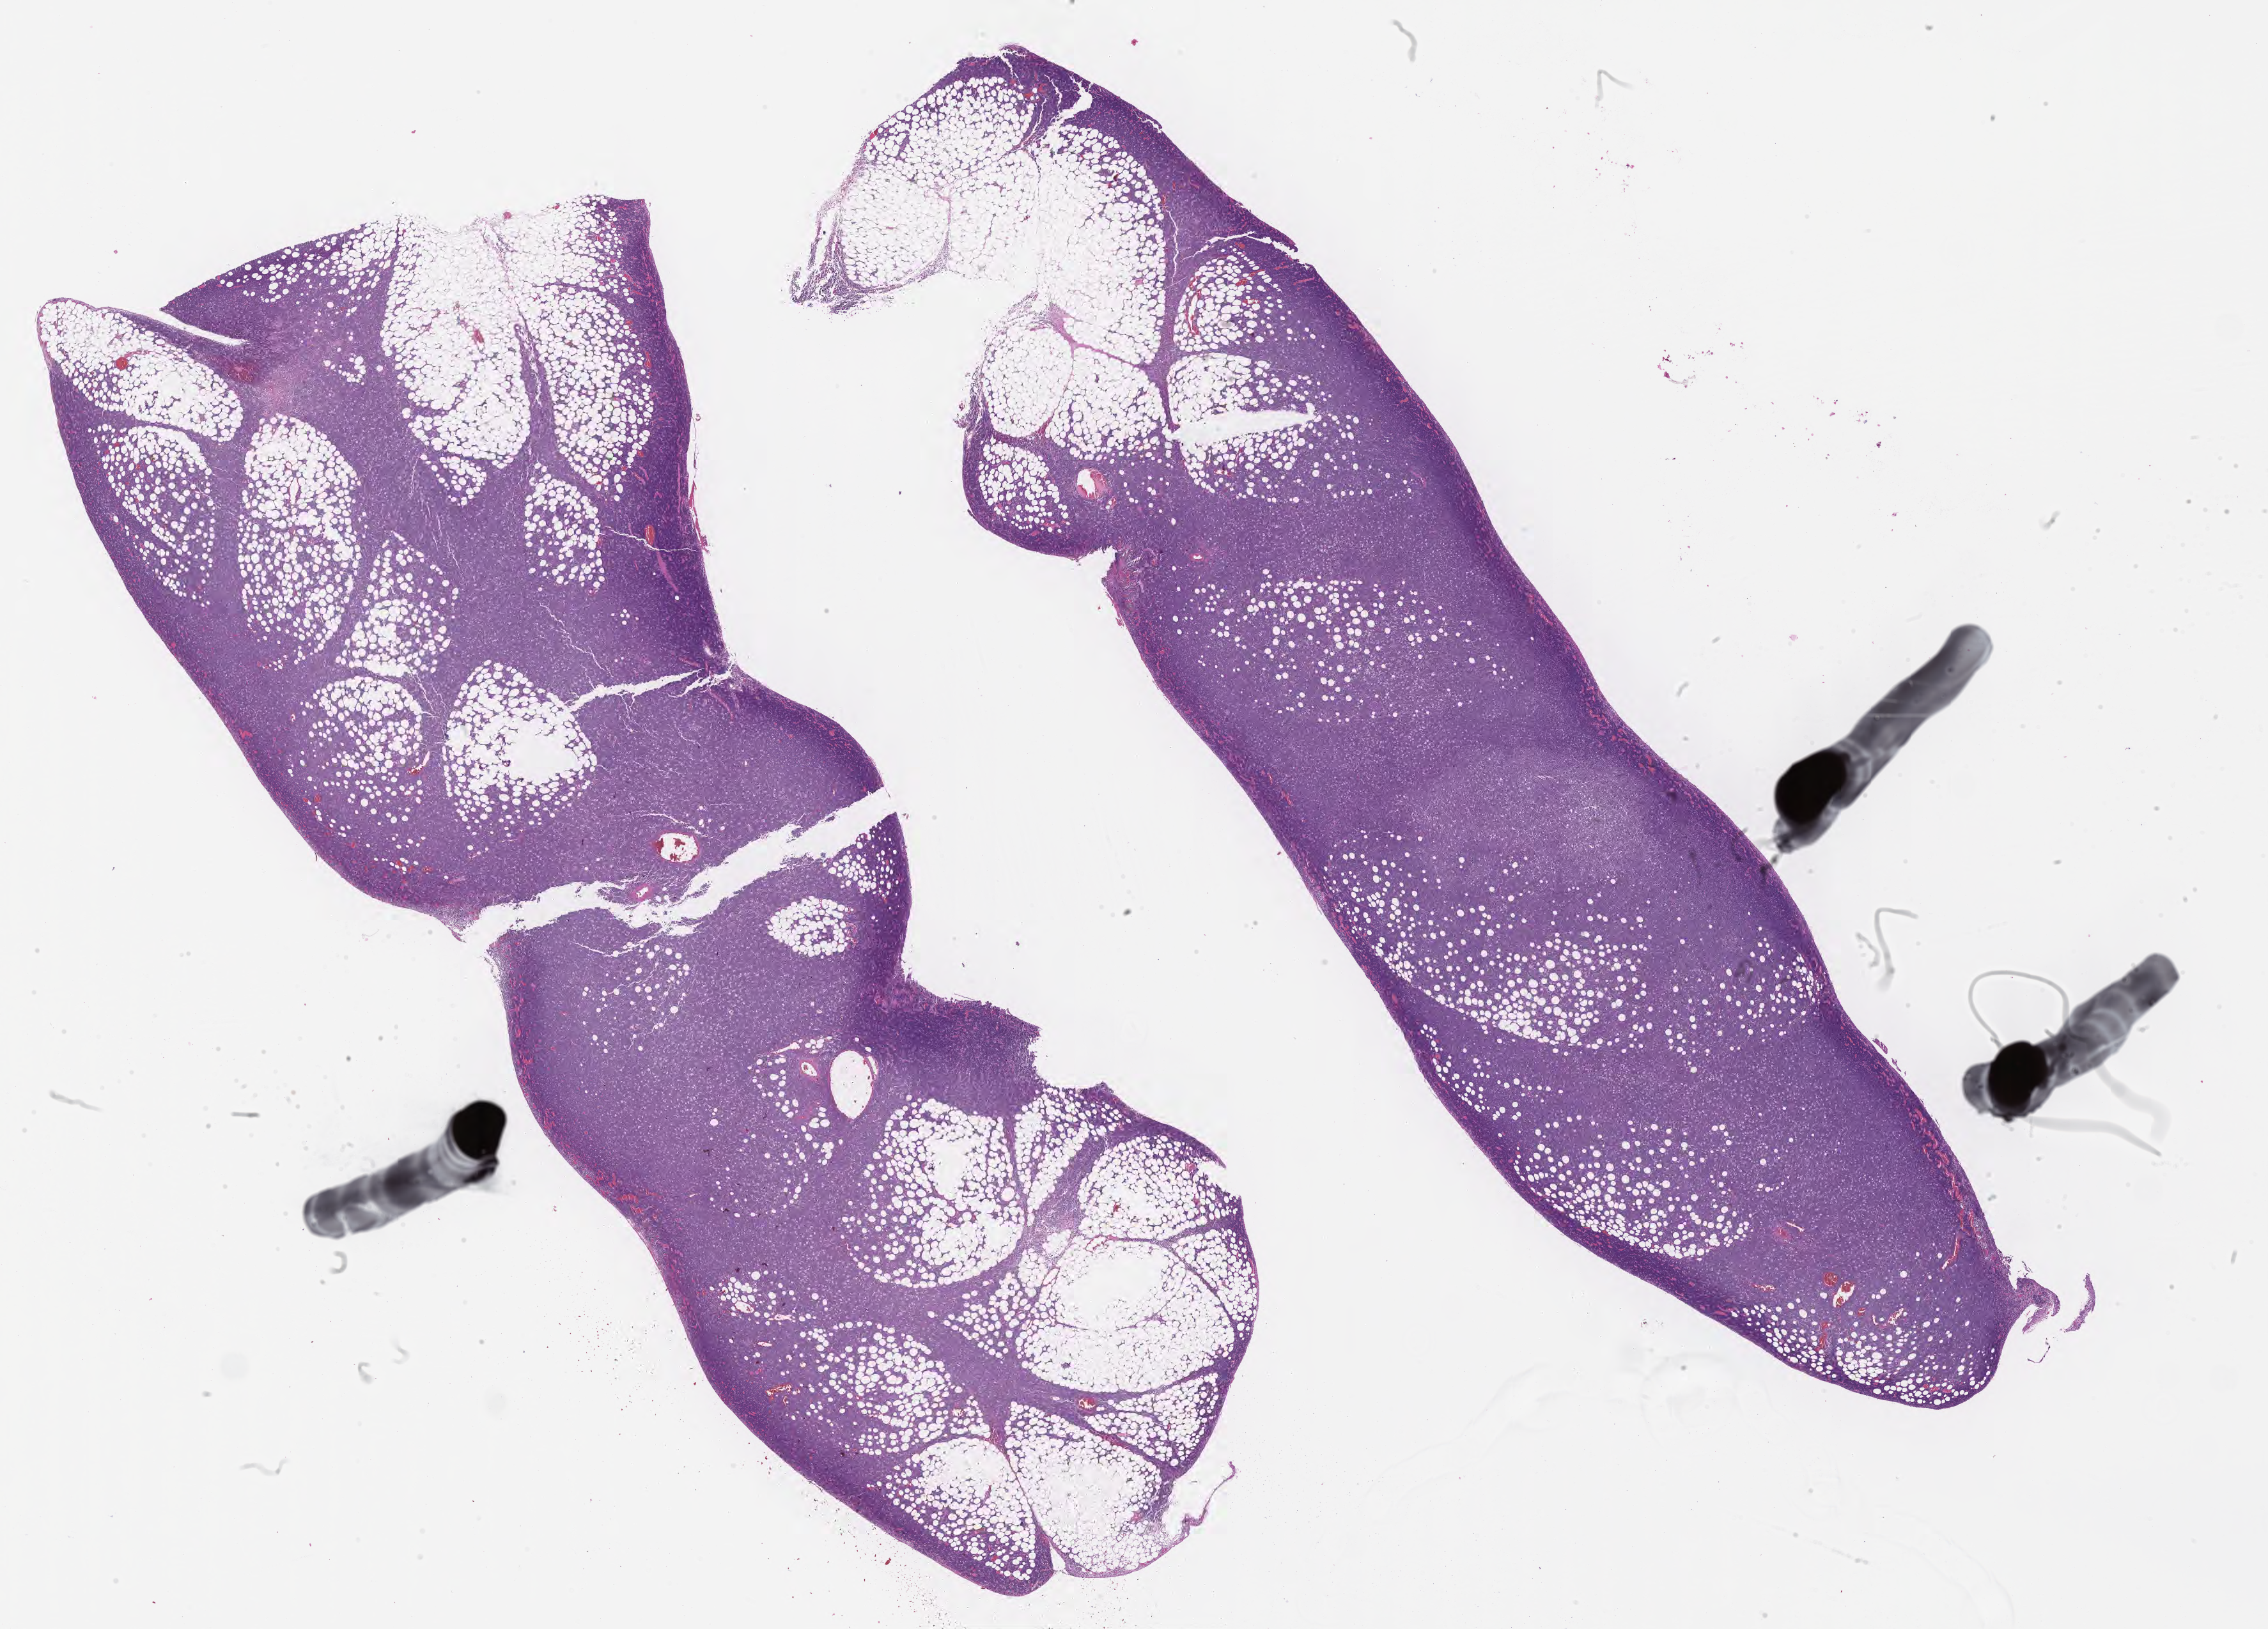
Whole-slide image, hematoxylin and eosin (H&E) stain, shown as a low-resolution overview of the whole scanned area (about 28.7 x 20.6 mm), tumor tissue. Male patient, aged 32.
* diagnosis: Burkitt lymphoma, NOS